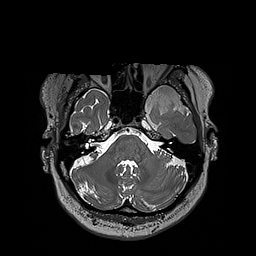
Brain MRI from a brain-tumour surgery series, one axial slice. Position 149 of 192 along the scan axis. 1 mm slice thickness. 256 × 256 image matrix, field of view 250 × 250 mm. Case-level facts recorded for this patient, not image findings: histopathology: Oligodendroglioma; WHO grade: 3; IDH mutation: yes; tumour location: Left Sylvian Fissure (Temporal).
Structures marked on this image (expert manual segmentation):
- tumour: bounding box (x1, y1, x2, y2) in pixels: (124, 85, 197, 112)